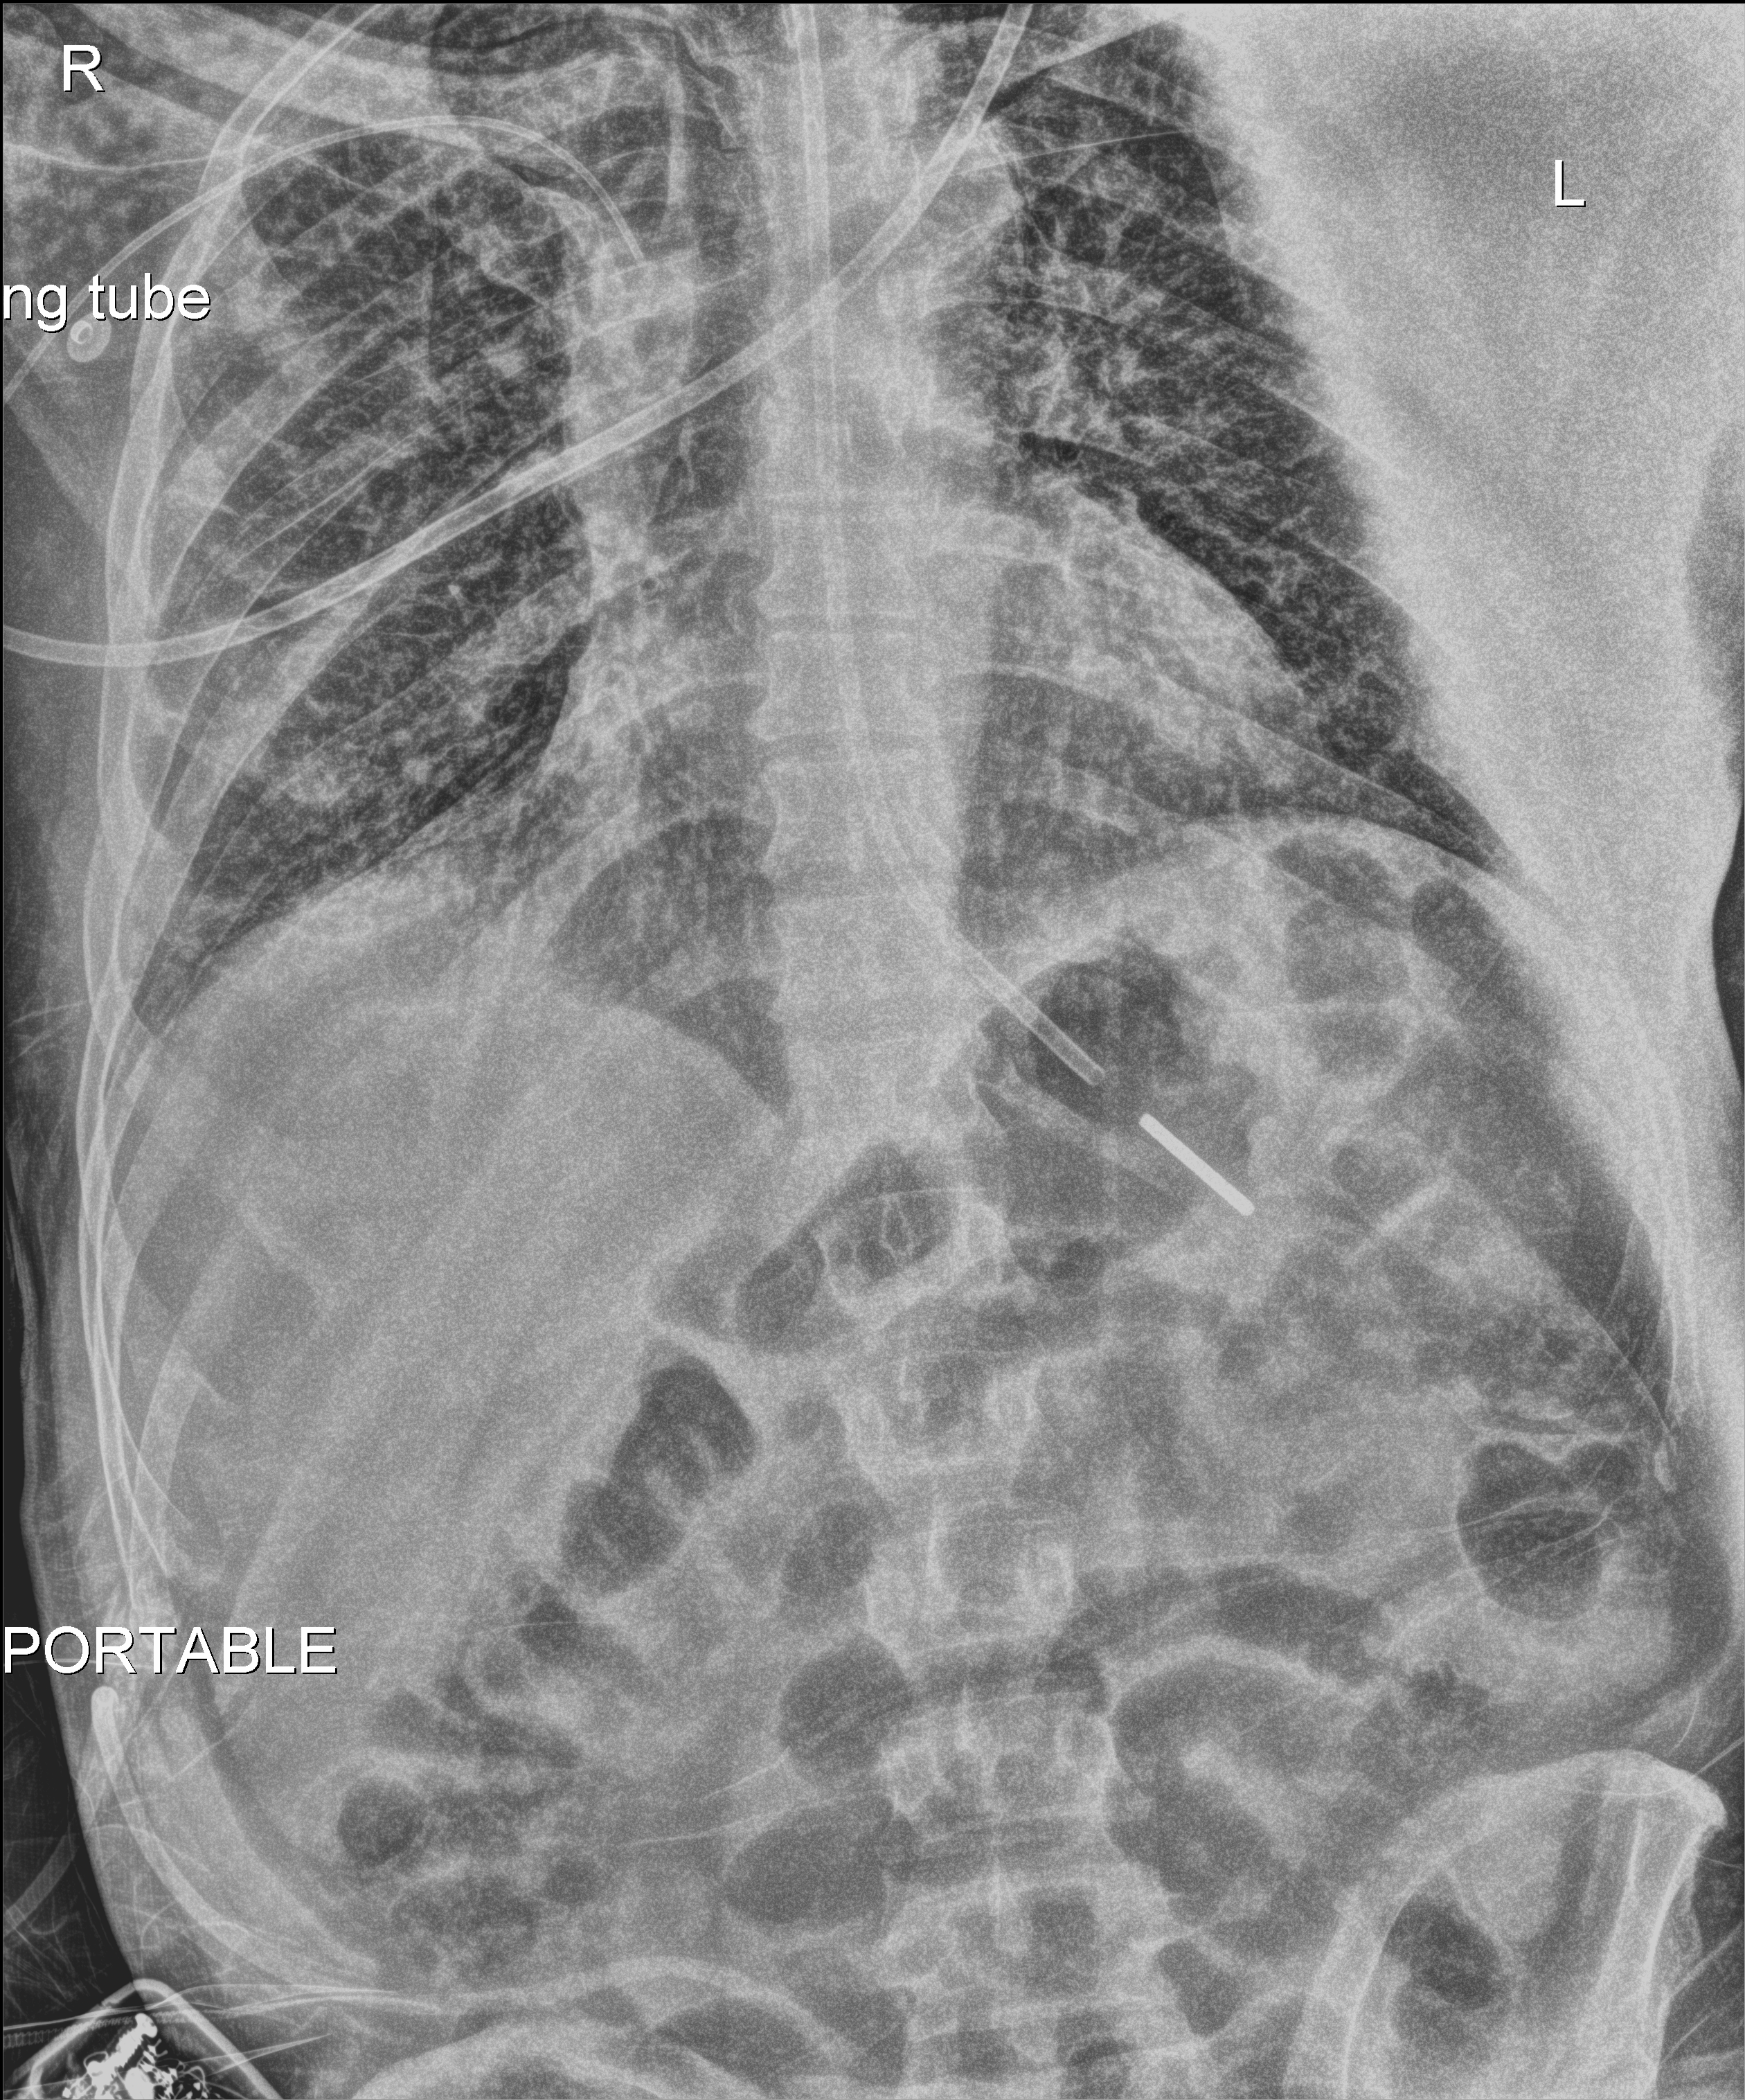
Bedside chest radiograph (digital radiography), anteroposterior (AP) projection. Male patient hospitalised with COVID-19, age 18–59 years.
Hospital-stay facts (about this admission, not read from this image; timing relative to this image not recorded): chronic kidney disease (admission record): no; length of hospital stay: 41 days.